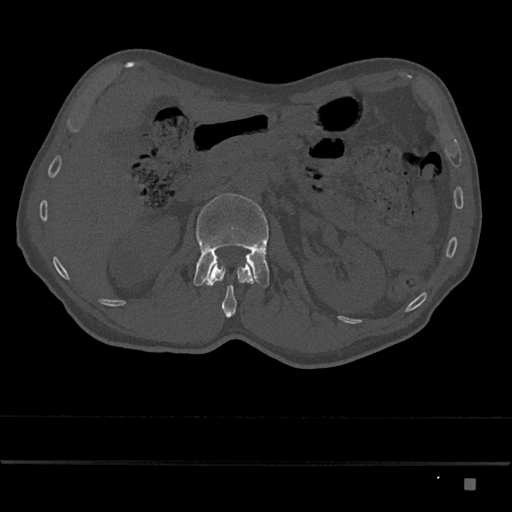
CT including the spine, one axial slice. Slice 504 of 797 in the series (ordered by position). Reconstruction kernel Br40s/3. 120 kVp. Bone window (W 1800 / L 400 HU). 0.5 mm slice thickness. 512 × 512 image matrix, field of view 390 × 390 mm. Male patient, age 72 years. Case-level facts recorded for this patient, not image findings: primary cancer: prostate.
Structures marked on this image (semi-automatic segmentation, software-assisted and operator-edited):
- L1 vertebra: bounding box (x1, y1, x2, y2) in pixels: (206, 262, 256, 318)
- L2 vertebra: (193, 193, 270, 287)